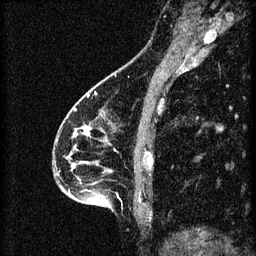
Breast MRI (dynamic contrast-enhanced), one sagittal slice. Position 27 of 60 along the scan axis. 3 images stored at this slice position (order not interpretable as contrast timing). 1.5 T. TE 4.2 ms, TR 8.2 ms. 2 mm slice thickness. 256 × 256 image matrix. Patient: female, 46 years.
Annotated regions visible in this slice (semi-automatically segmented with operator editing):
- analysis volume of interest (the breast-tissue region the enhancement analysis was run in; not a lesion): bounding box <55,114,148,209> (left, top, right, bottom; pixels)
- tumour enhancement mask (voxels above the 70 % enhancement threshold inside the analysis volume of interest): <75,126,91,137>